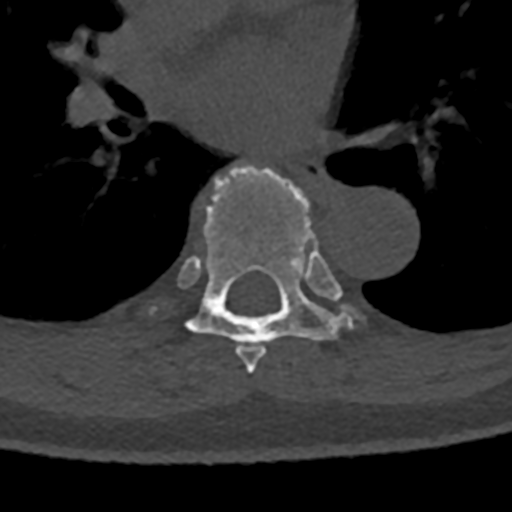
CT including the spine, one axial slice; slice 769 of 797 in the series (ordered by position); bone window (W 1800 / L 400 HU); 0.5 mm slice thickness; 512 × 512 image matrix, field of view 160 × 160 mm. Patient: male, 74 years. Case-level facts recorded for this patient, not image findings: primary cancer: renal; vertebrae with lytic lesions (as recorded): T10, L1, L2, L3, L4, L5.
Annotated regions visible in this slice (semi-automatic segmentation, software-assisted and operator-edited):
- T6 vertebra: box from (x=237, y=344) to (x=266, y=374) px
- T7 vertebra: (x=156, y=164)–(x=359, y=364)